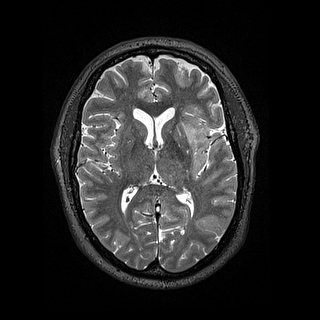
Brain MRI from a brain-tumour surgery series, one axial slice; slice 80 of 144 in the series (ordered by position); 320 × 320 image matrix, field of view 254 × 254 mm. From the clinical record (not read from this slice): histopathology: Astrocytoma; WHO grade: 2; IDH mutation: yes.
Structures marked on this image (outlined manually by an expert reader):
- tumour: bounding box <183,124,211,177> (left, top, right, bottom; pixels)